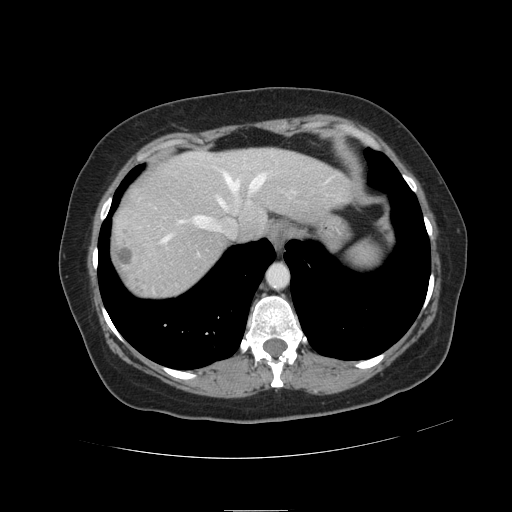
Contrast-enhanced abdominal CT, one axial slice. Position 100 of 121 along the scan axis. Intravenous contrast given. Soft-tissue window (W 400 / L 40 HU). 512 × 512 image matrix, field of view 400 × 400 mm. Female patient, age 52 years. Case-level facts recorded for this patient, not image findings: diagnosis: colorectal cancer liver metastases, imaged before liver resection; multiple liver metastases: yes; largest metastasis: 6.3 cm; disease in both lobes: no.
Structures marked on this image (expert manual segmentation):
- hepatic veins: bounding box <162,174,265,255> (left, top, right, bottom; pixels)
- liver: <111,149,349,299>
- planned liver remnant (the part of the liver to remain after resection): <172,149,349,240>
- liver metastasis: <115,246,134,270>